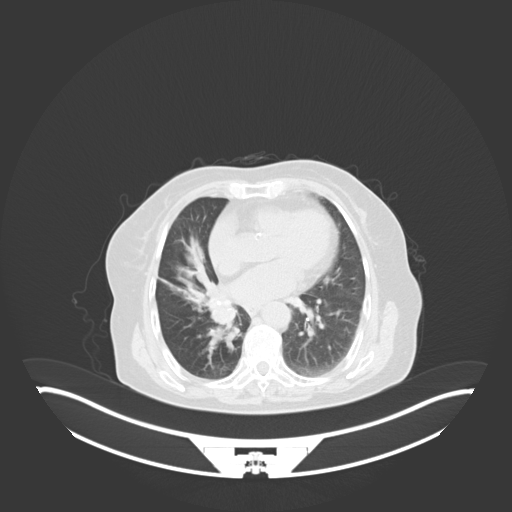
Chest CT, one axial slice; reconstruction kernel B30f; lung window (W 1500 / L -600 HU); 512 × 512 image matrix, field of view 500 × 500 mm. Patient: female, 75 years. From the clinical record (not read from this slice): clinical TNM (as recorded): T1b N0 M1a.
Annotated regions visible in this slice (rectangle marked by the reading radiologist):
- lung tumour (recorded histology: squamous cell carcinoma): bounding box <203,300,239,348> (left, top, right, bottom; pixels)